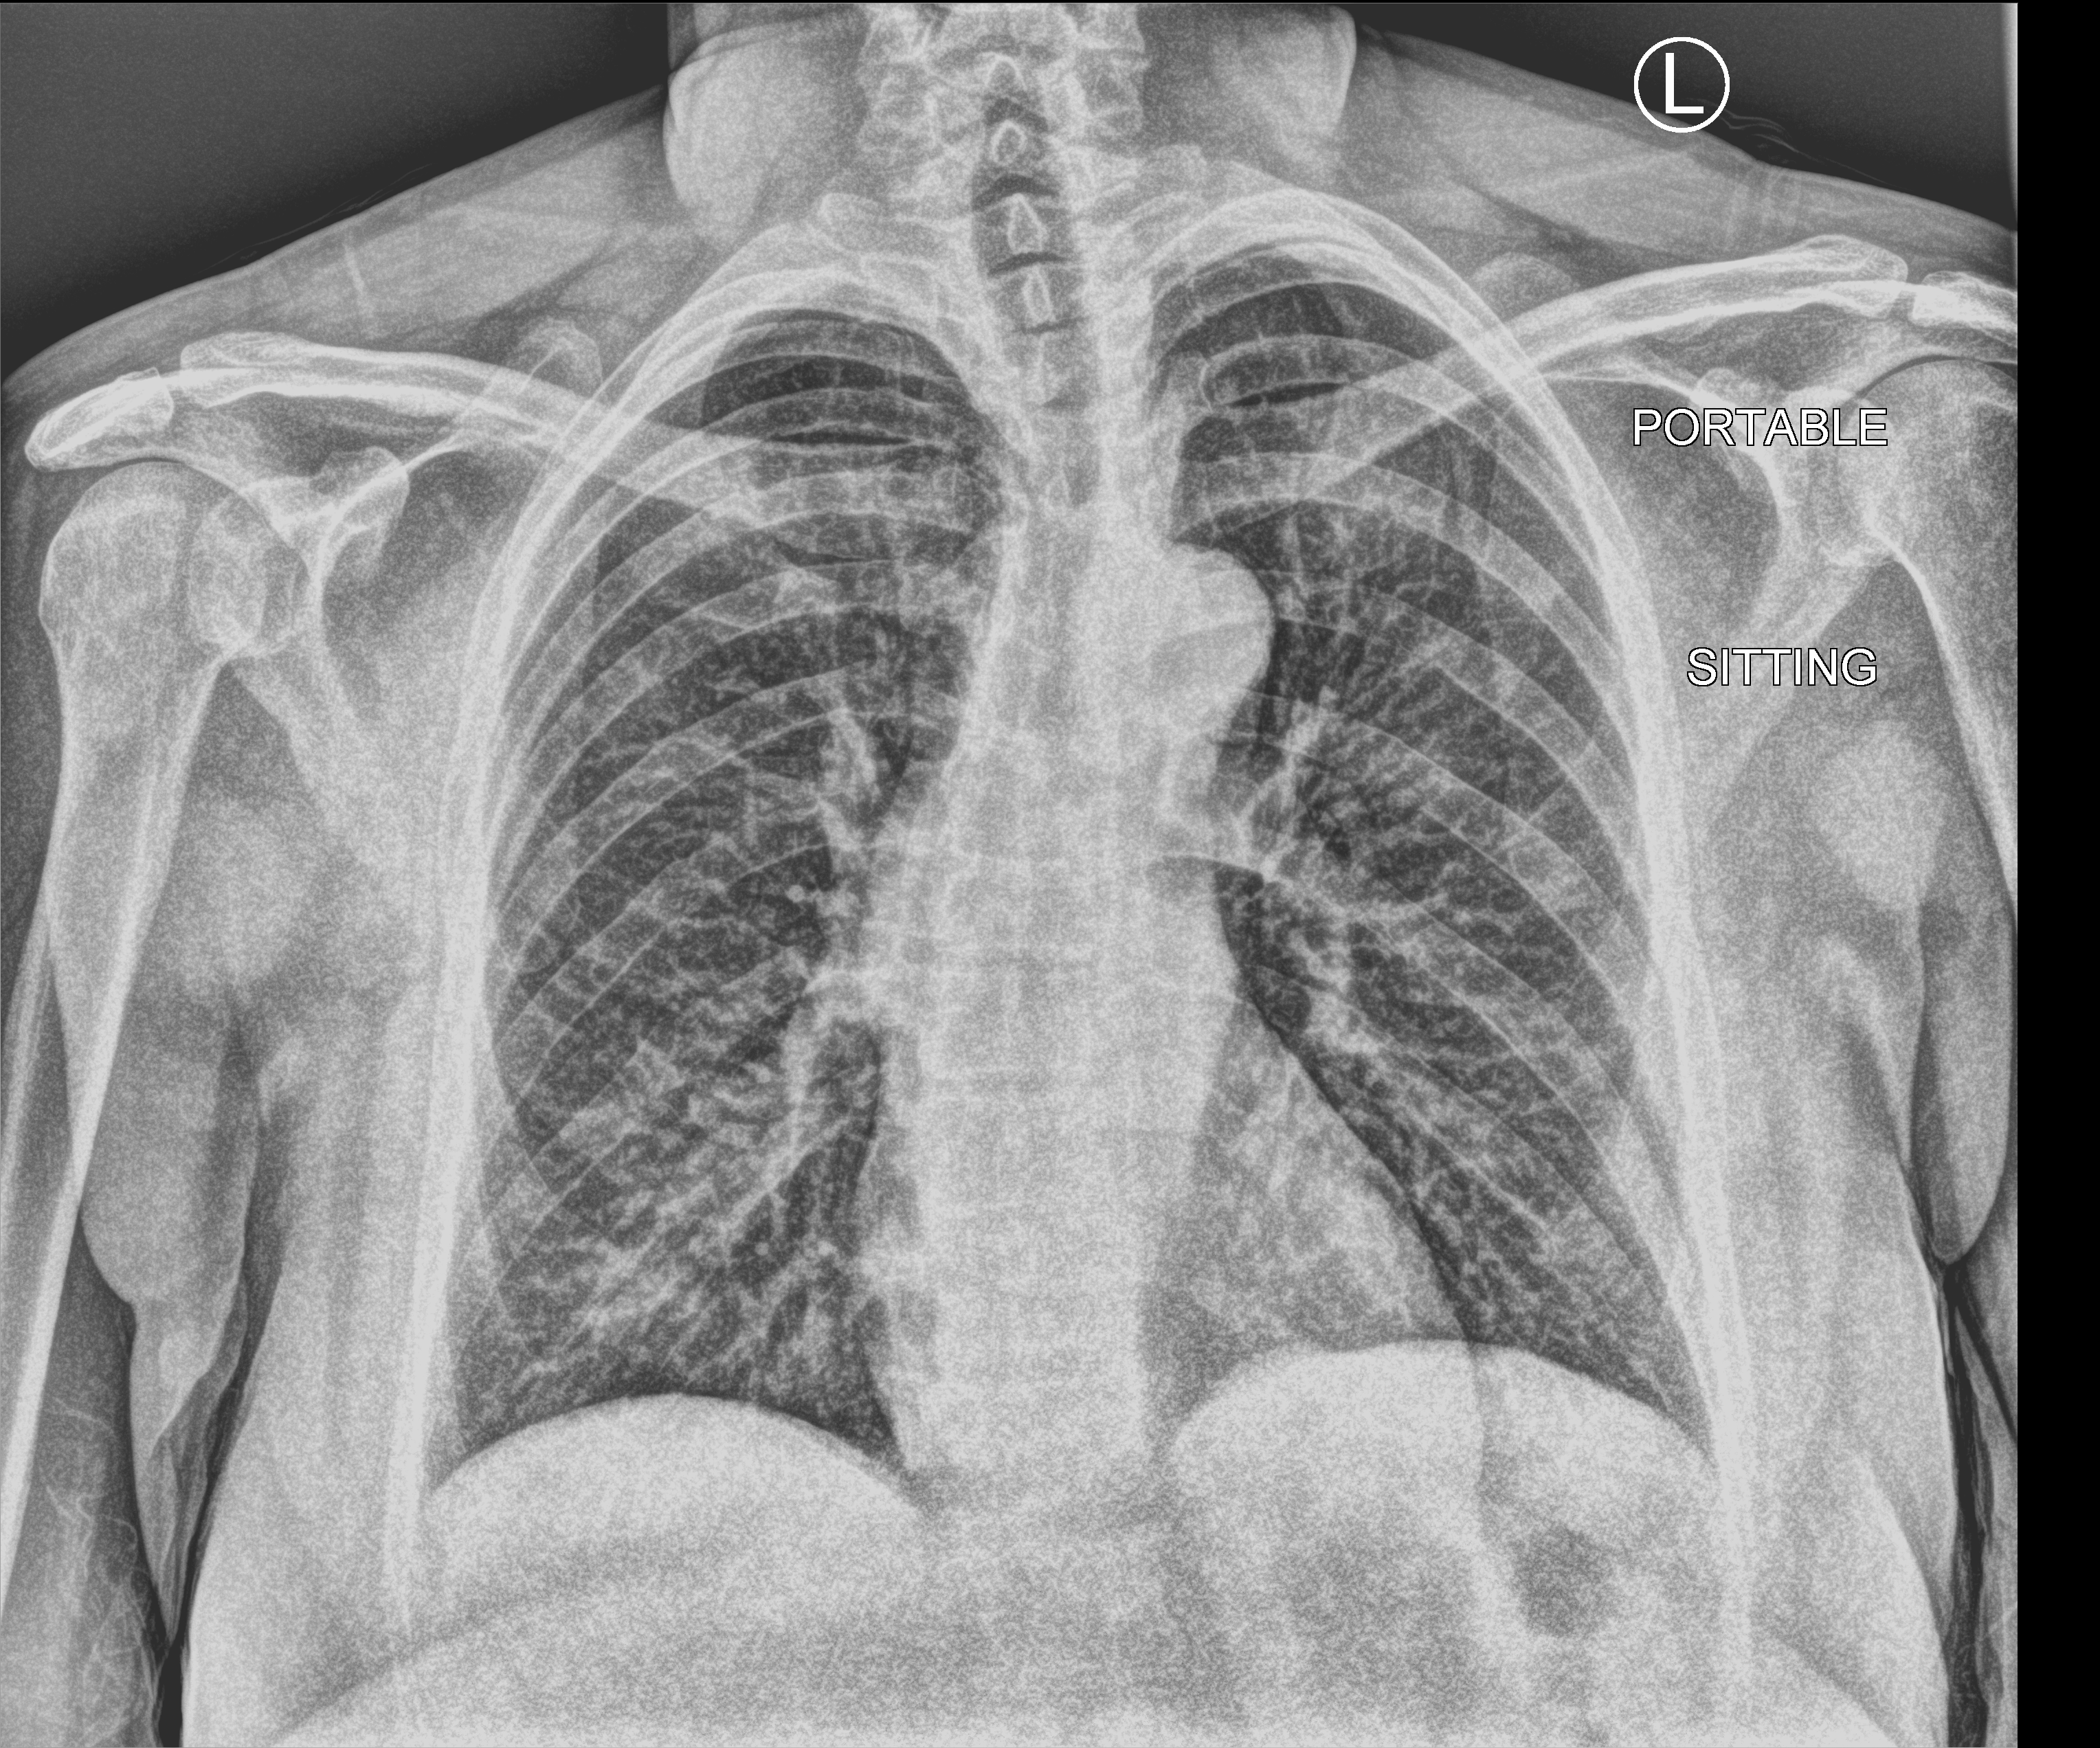
Chest X-ray (portable). Female patient hospitalised with COVID-19, age 18–59 years.
Admission-level facts for this patient (not findings on this image; timing relative to this image not recorded): length of hospital stay: 1 day; mechanically ventilated during this hospital stay: no; admitted to intensive care during this hospital stay: no.